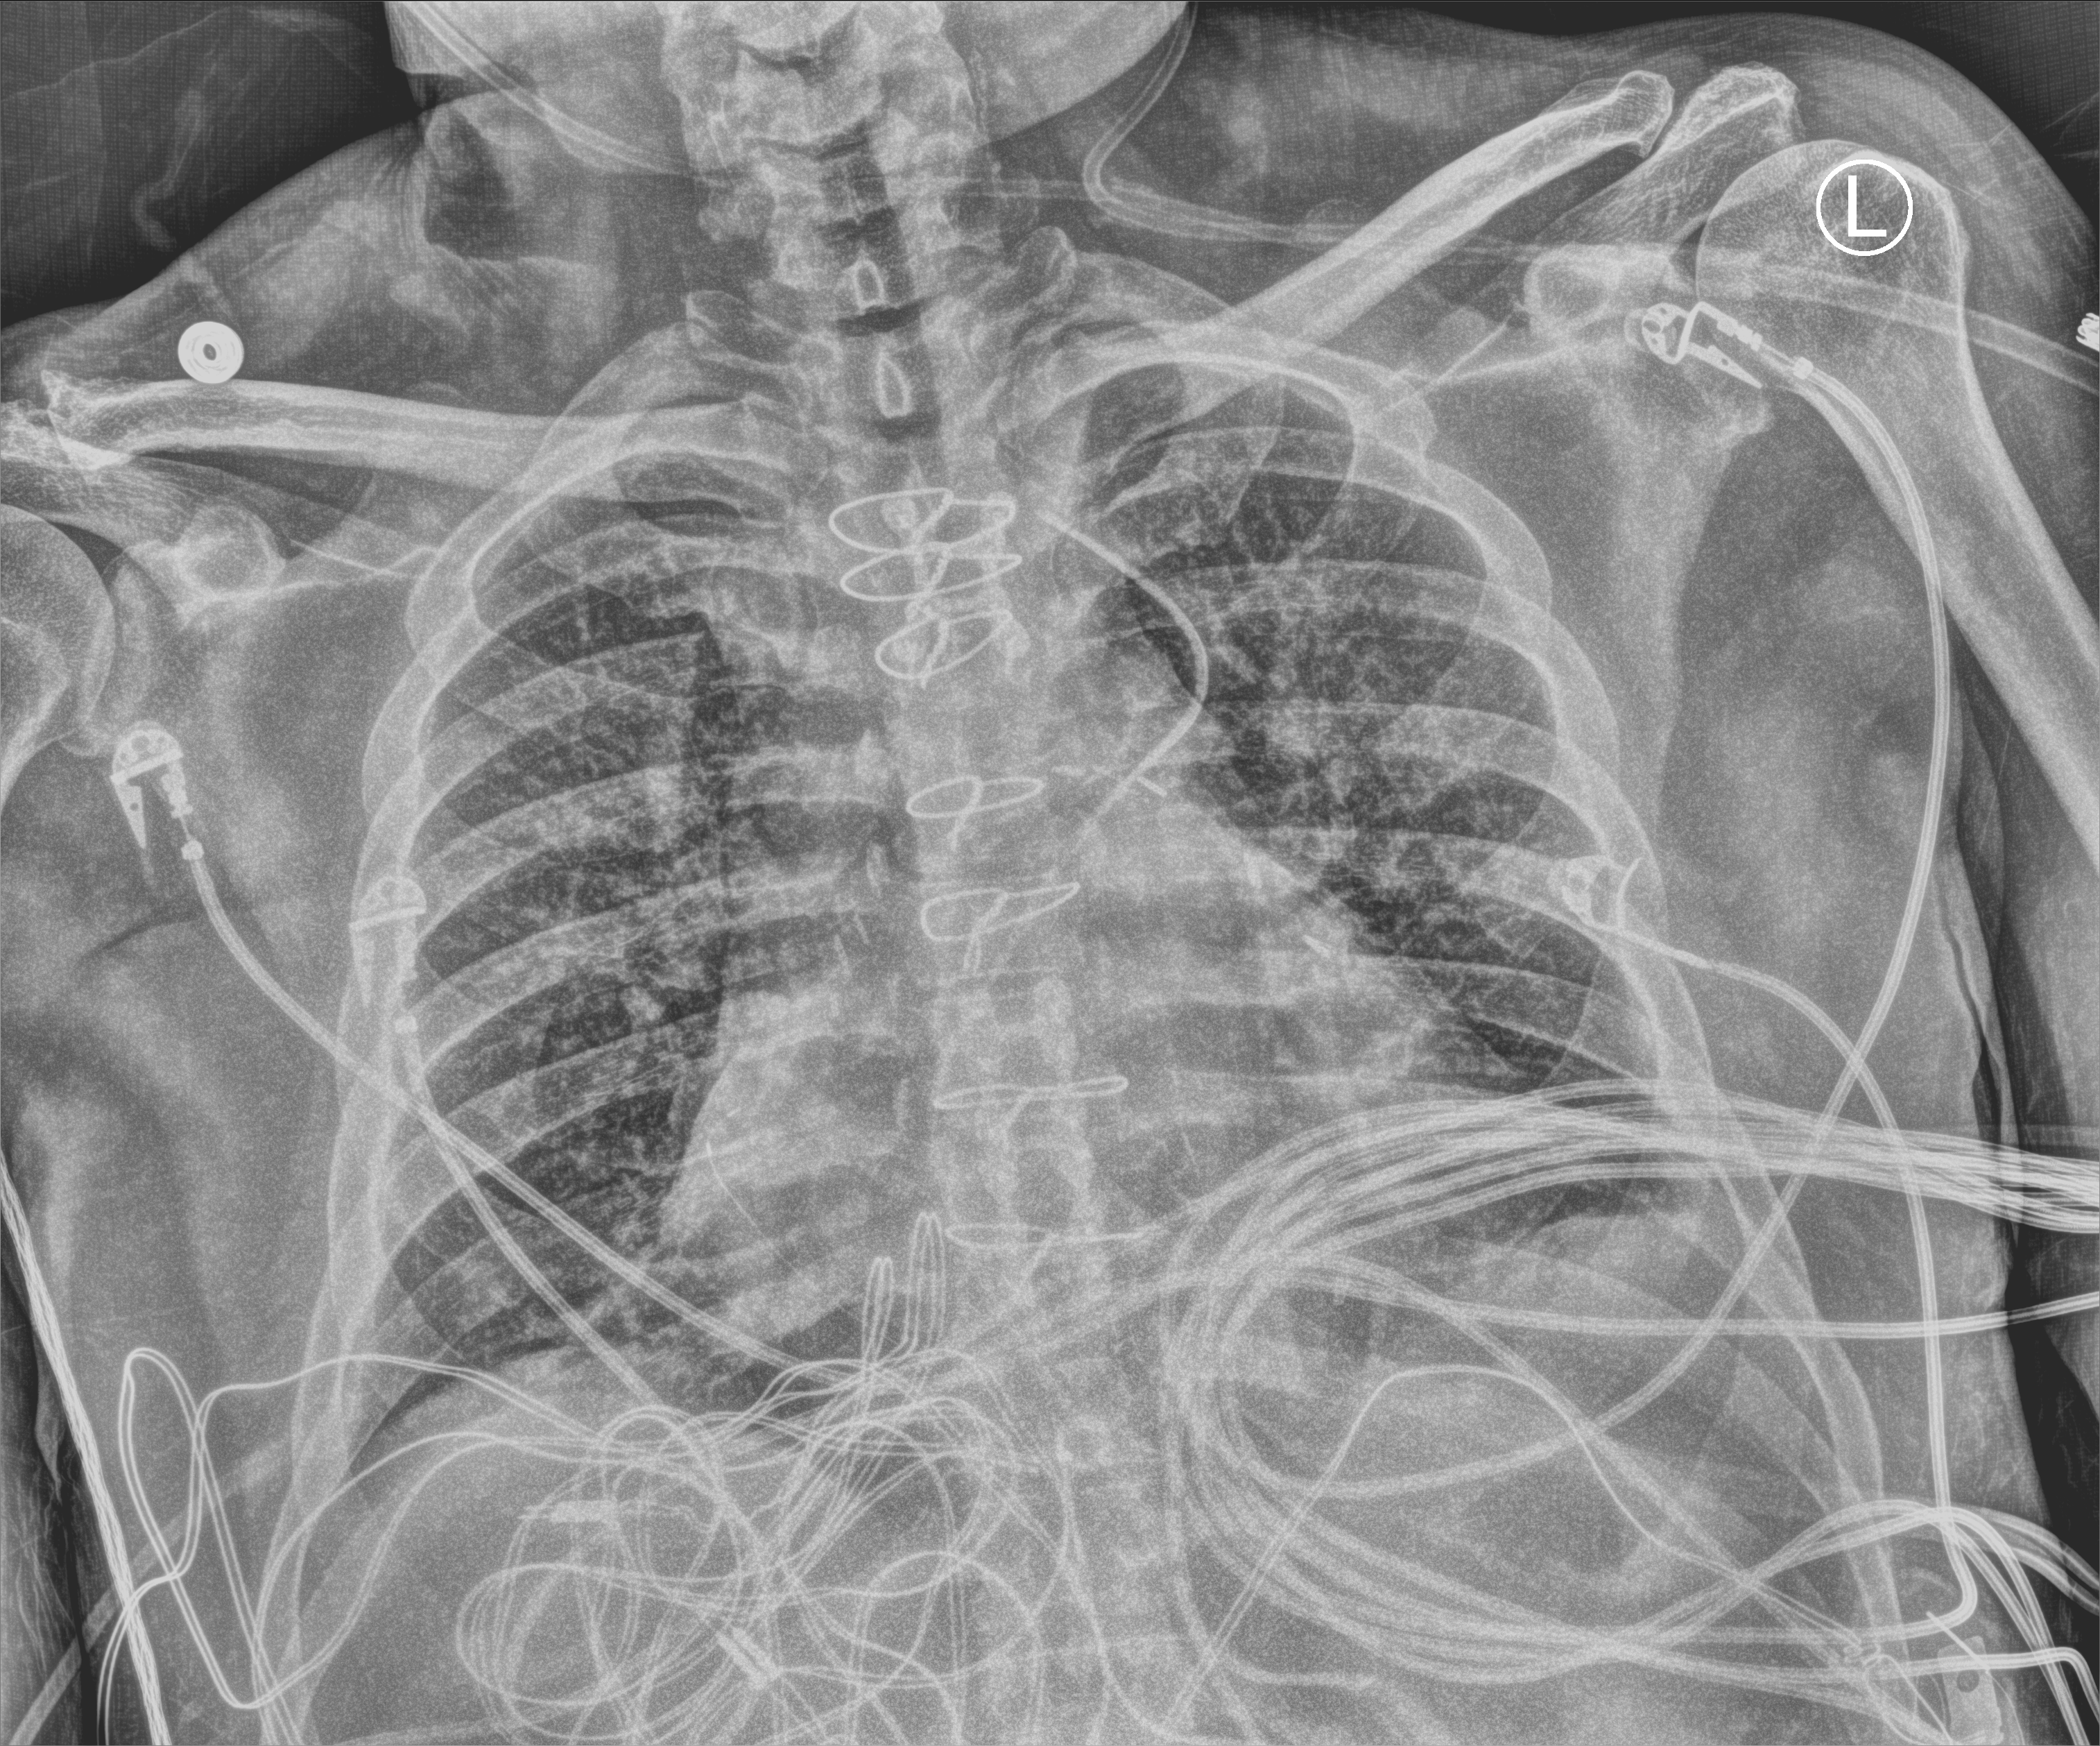
Bedside chest radiograph (computed radiography), anteroposterior (AP) projection. Male patient hospitalised with COVID-19, age 60–74 years.
From the hospital-stay record, not from the radiograph (when in the stay this image was taken is not recorded): mechanically ventilated during this hospital stay: no; admitted to intensive care during this hospital stay: no; hypertension (admission record): yes.